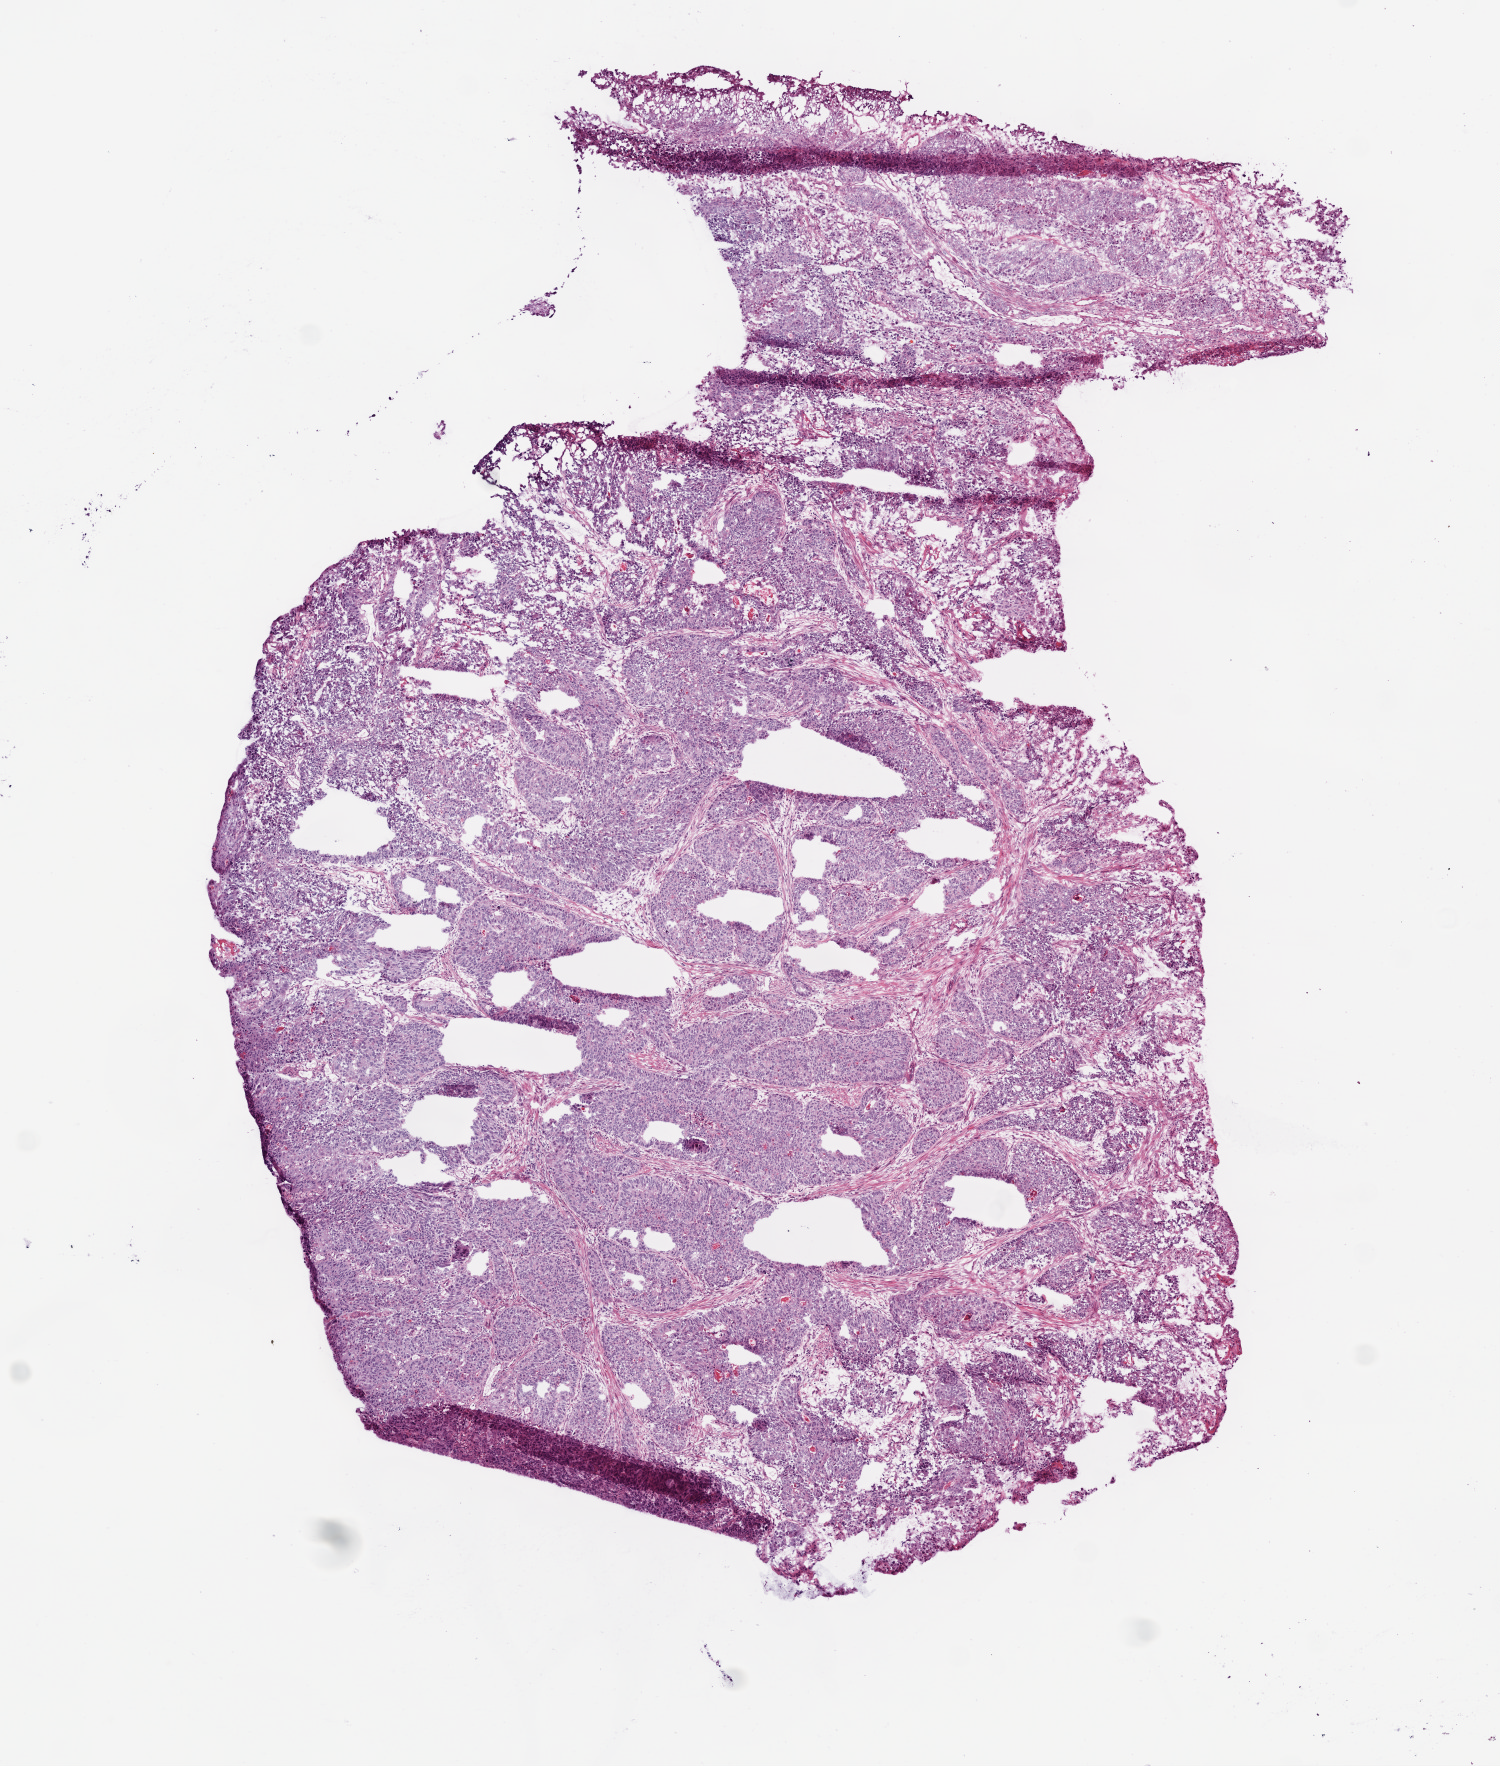
Whole-slide histology image, Hematoxylin and eosin (H&E) stained, whole scanned area (about 6.0 x 7.1 mm, acquisition: 20x scan) shown as a low-resolution overview. Frozen section. Colon, primary tumour sample. Patient: male, age at initial diagnosis 69 years. Composition of this section per pathologist review: tumour cells 80%, tumour nuclei 90%, normal cells 0%, stromal cells 10%, necrosis 10%.
Lymph nodes positive (case pathology): 4 of 18 examined. Pathologic diagnosis: Adenocarcinoma, NOS (sigmoid colon). AJCC pathologic stage: IIIC (6th edition).